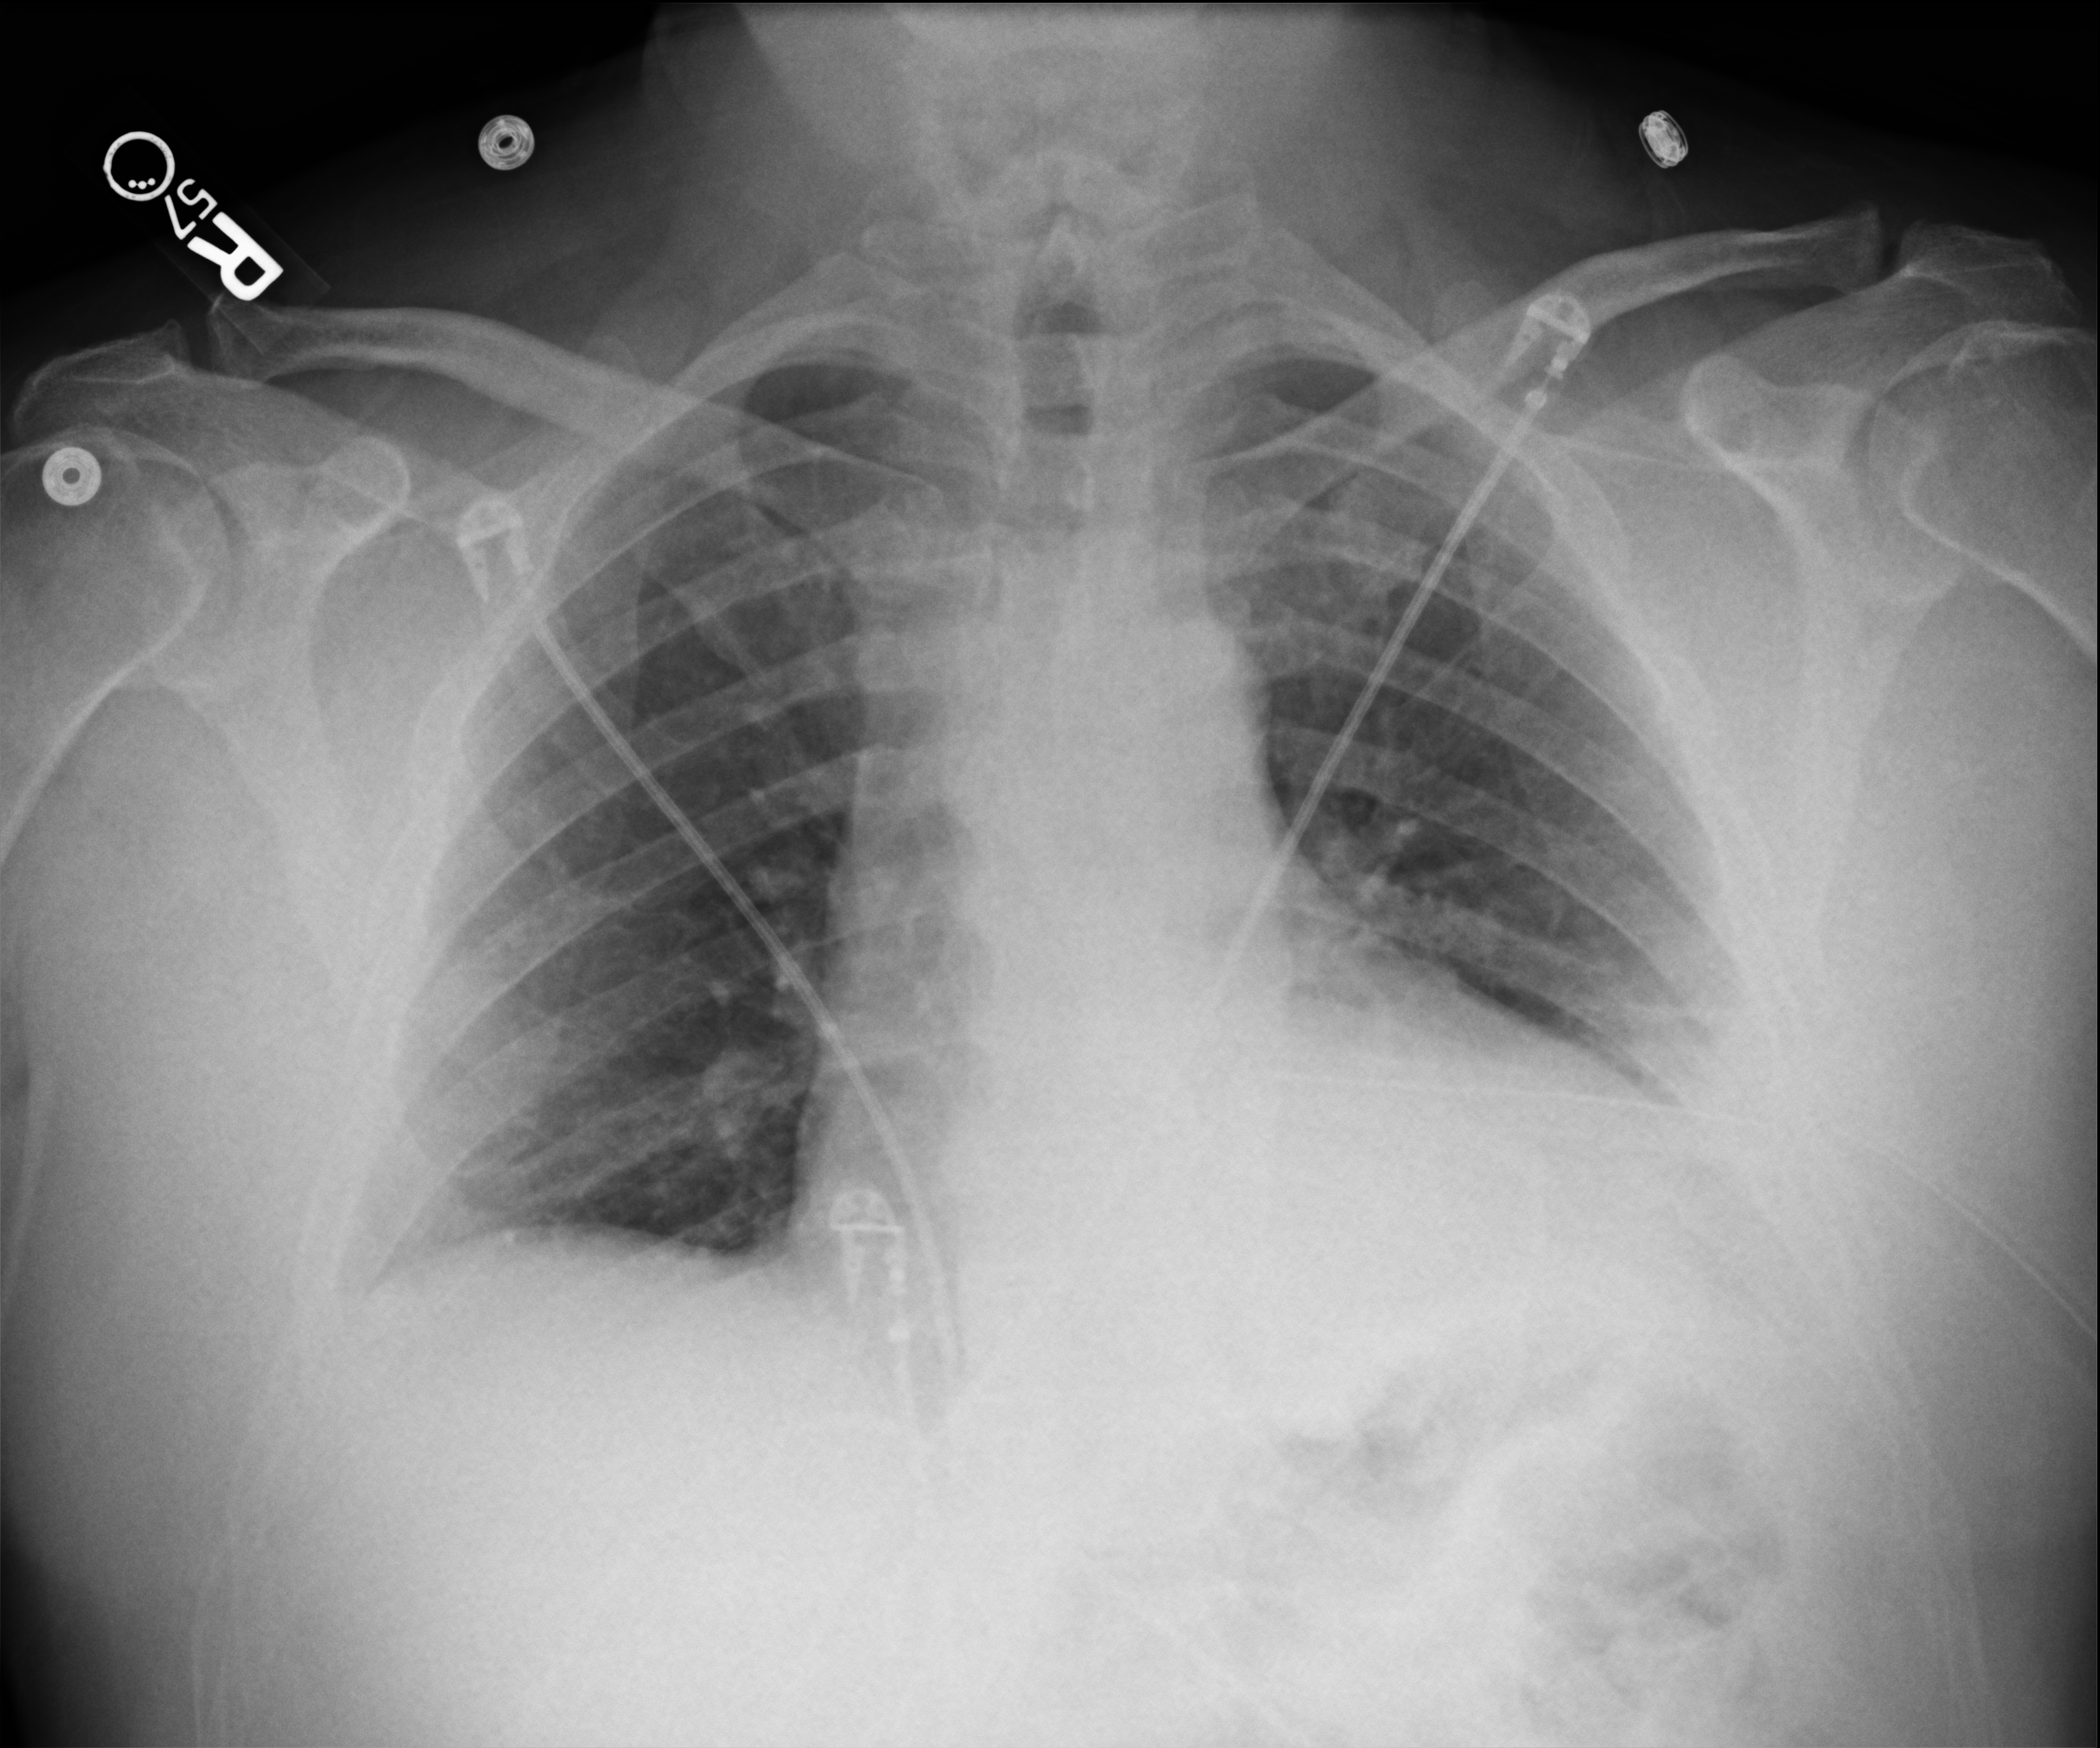
Chest X-ray (portable), anteroposterior (AP) projection. Patient hospitalised with COVID-19; male, aged 18–59 years.
From the hospital-stay record, not from the radiograph (when in the stay this image was taken is not recorded): length of hospital stay: 10 days.